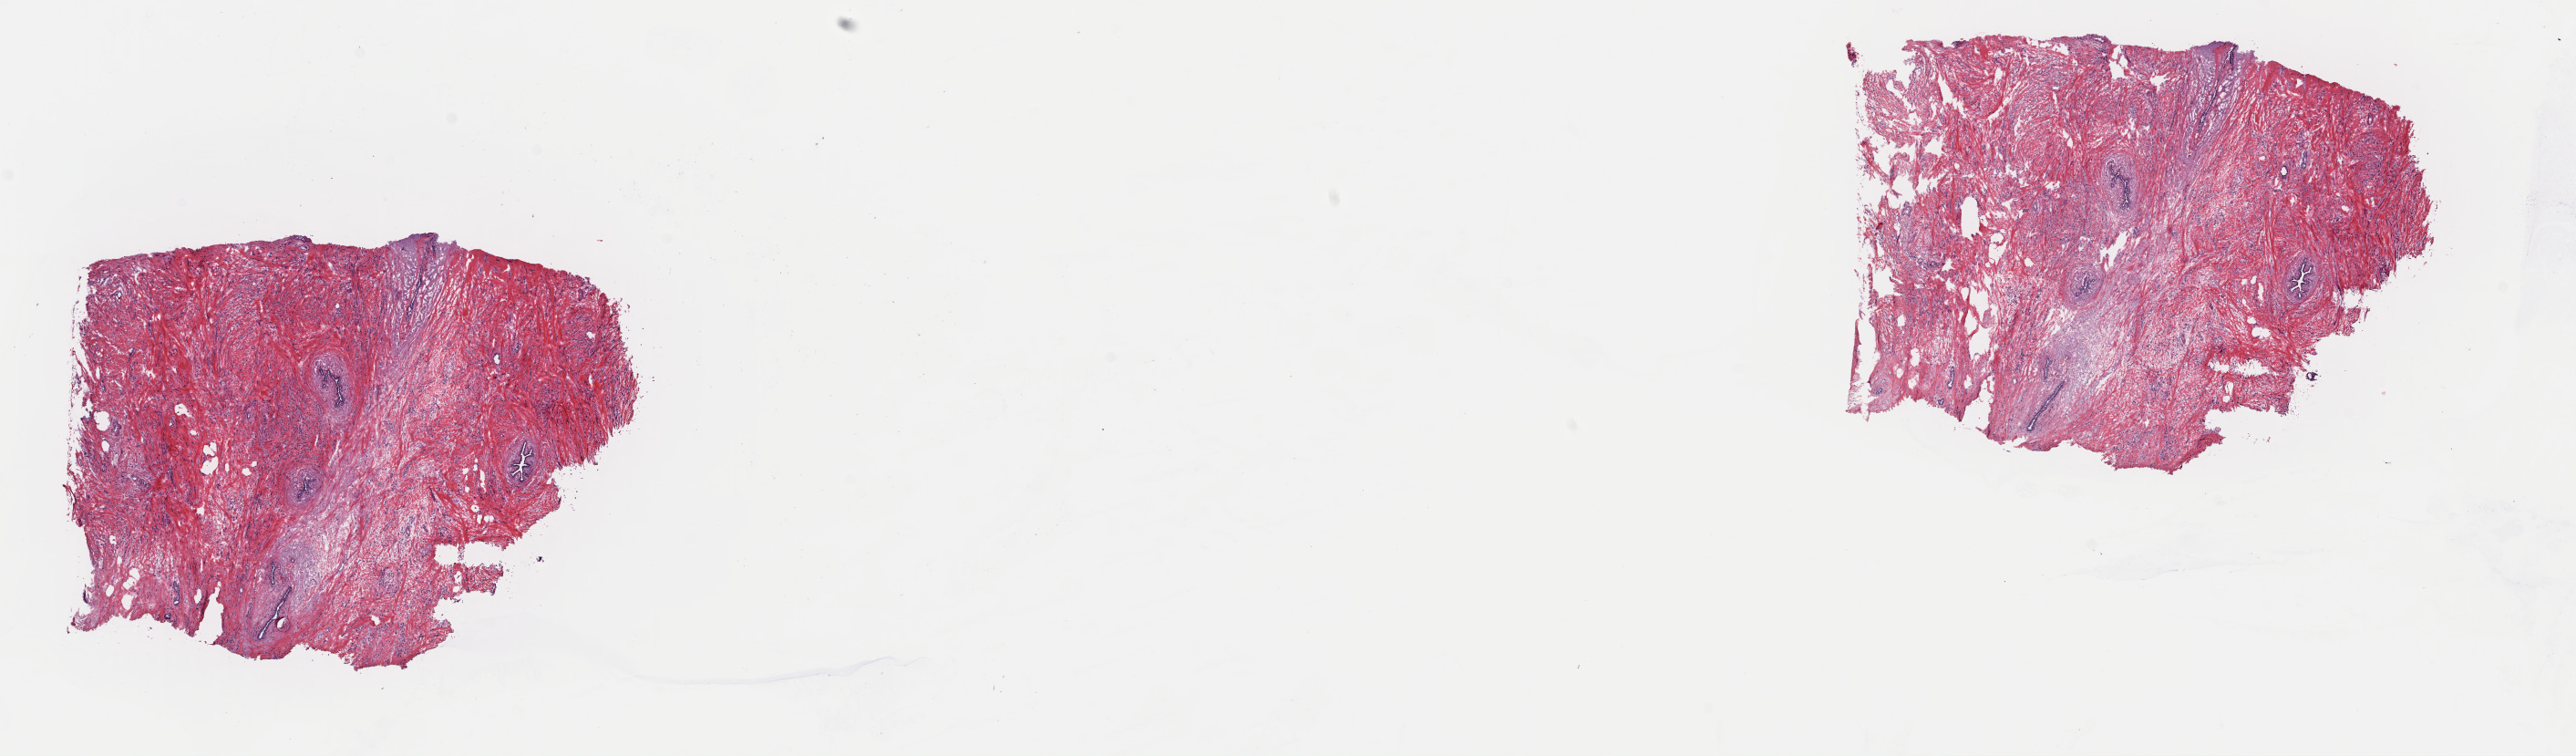
Hematoxylin and eosin (H&E) stained whole-slide image — shown as a low-resolution overview of the whole scanned area (about 22.3 x 6.5 mm). Frozen section from the top of the tissue portion. Primary tumour sample from the breast. Female, age 68 years at initial diagnosis. Slide review estimates, as recorded: tumour cells 90%, tumour nuclei 70%, normal cells 10%, stromal cells 0%, necrosis 0%. Inflammatory infiltration, as recorded: lymphocyte infiltration 0%, monocyte infiltration 0%, neutrophil infiltration 0%.
- AJCC pathologic stage: IA
- lymph nodes positive (case pathology): 0 of 1 examined
- histologic diagnosis: Lobular carcinoma, NOS